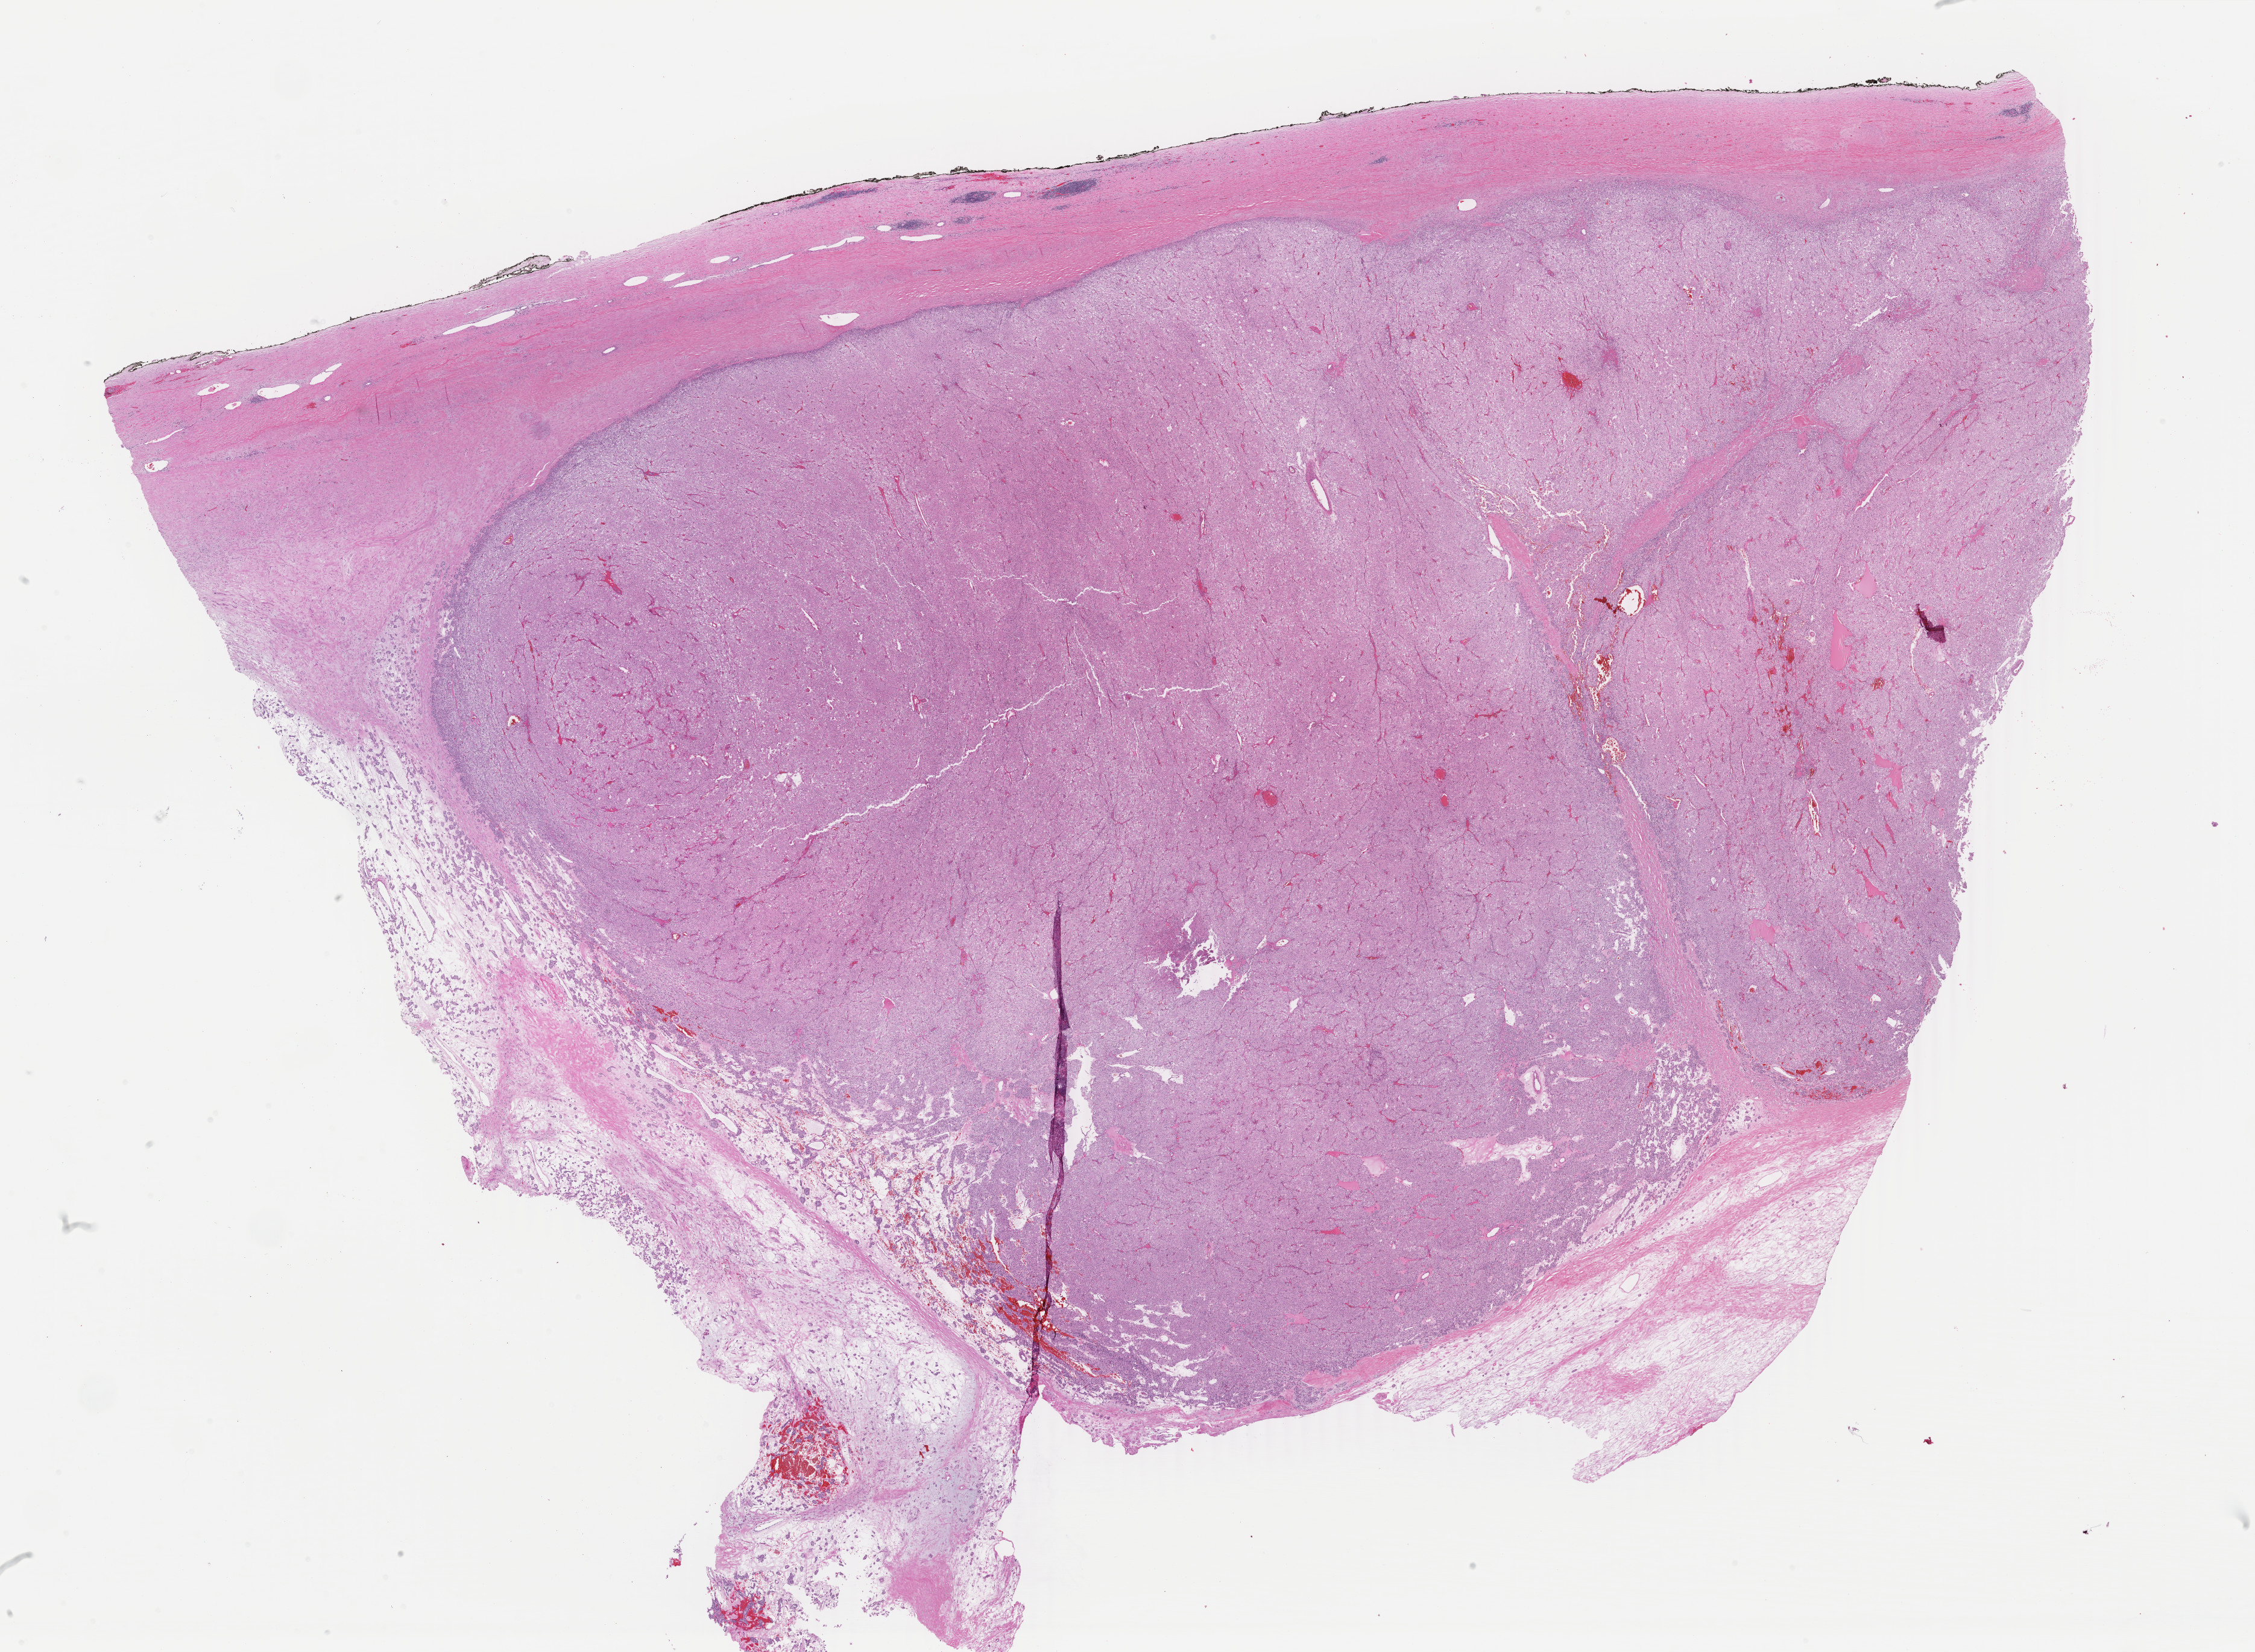
Hematoxylin and eosin (H&E) stained whole-slide image — whole scanned area (about 29.7 x 21.8 mm, slide scanned at 40x) shown as a low-resolution overview; formalin-fixed paraffin-embedded (FFPE) diagnostic section; primary tumour sample from the kidney. Patient: male, age at initial diagnosis 38 years.
Pathologic diagnosis: Renal cell carcinoma, chromophobe type. AJCC pathologic stage: II. Laterality: right.